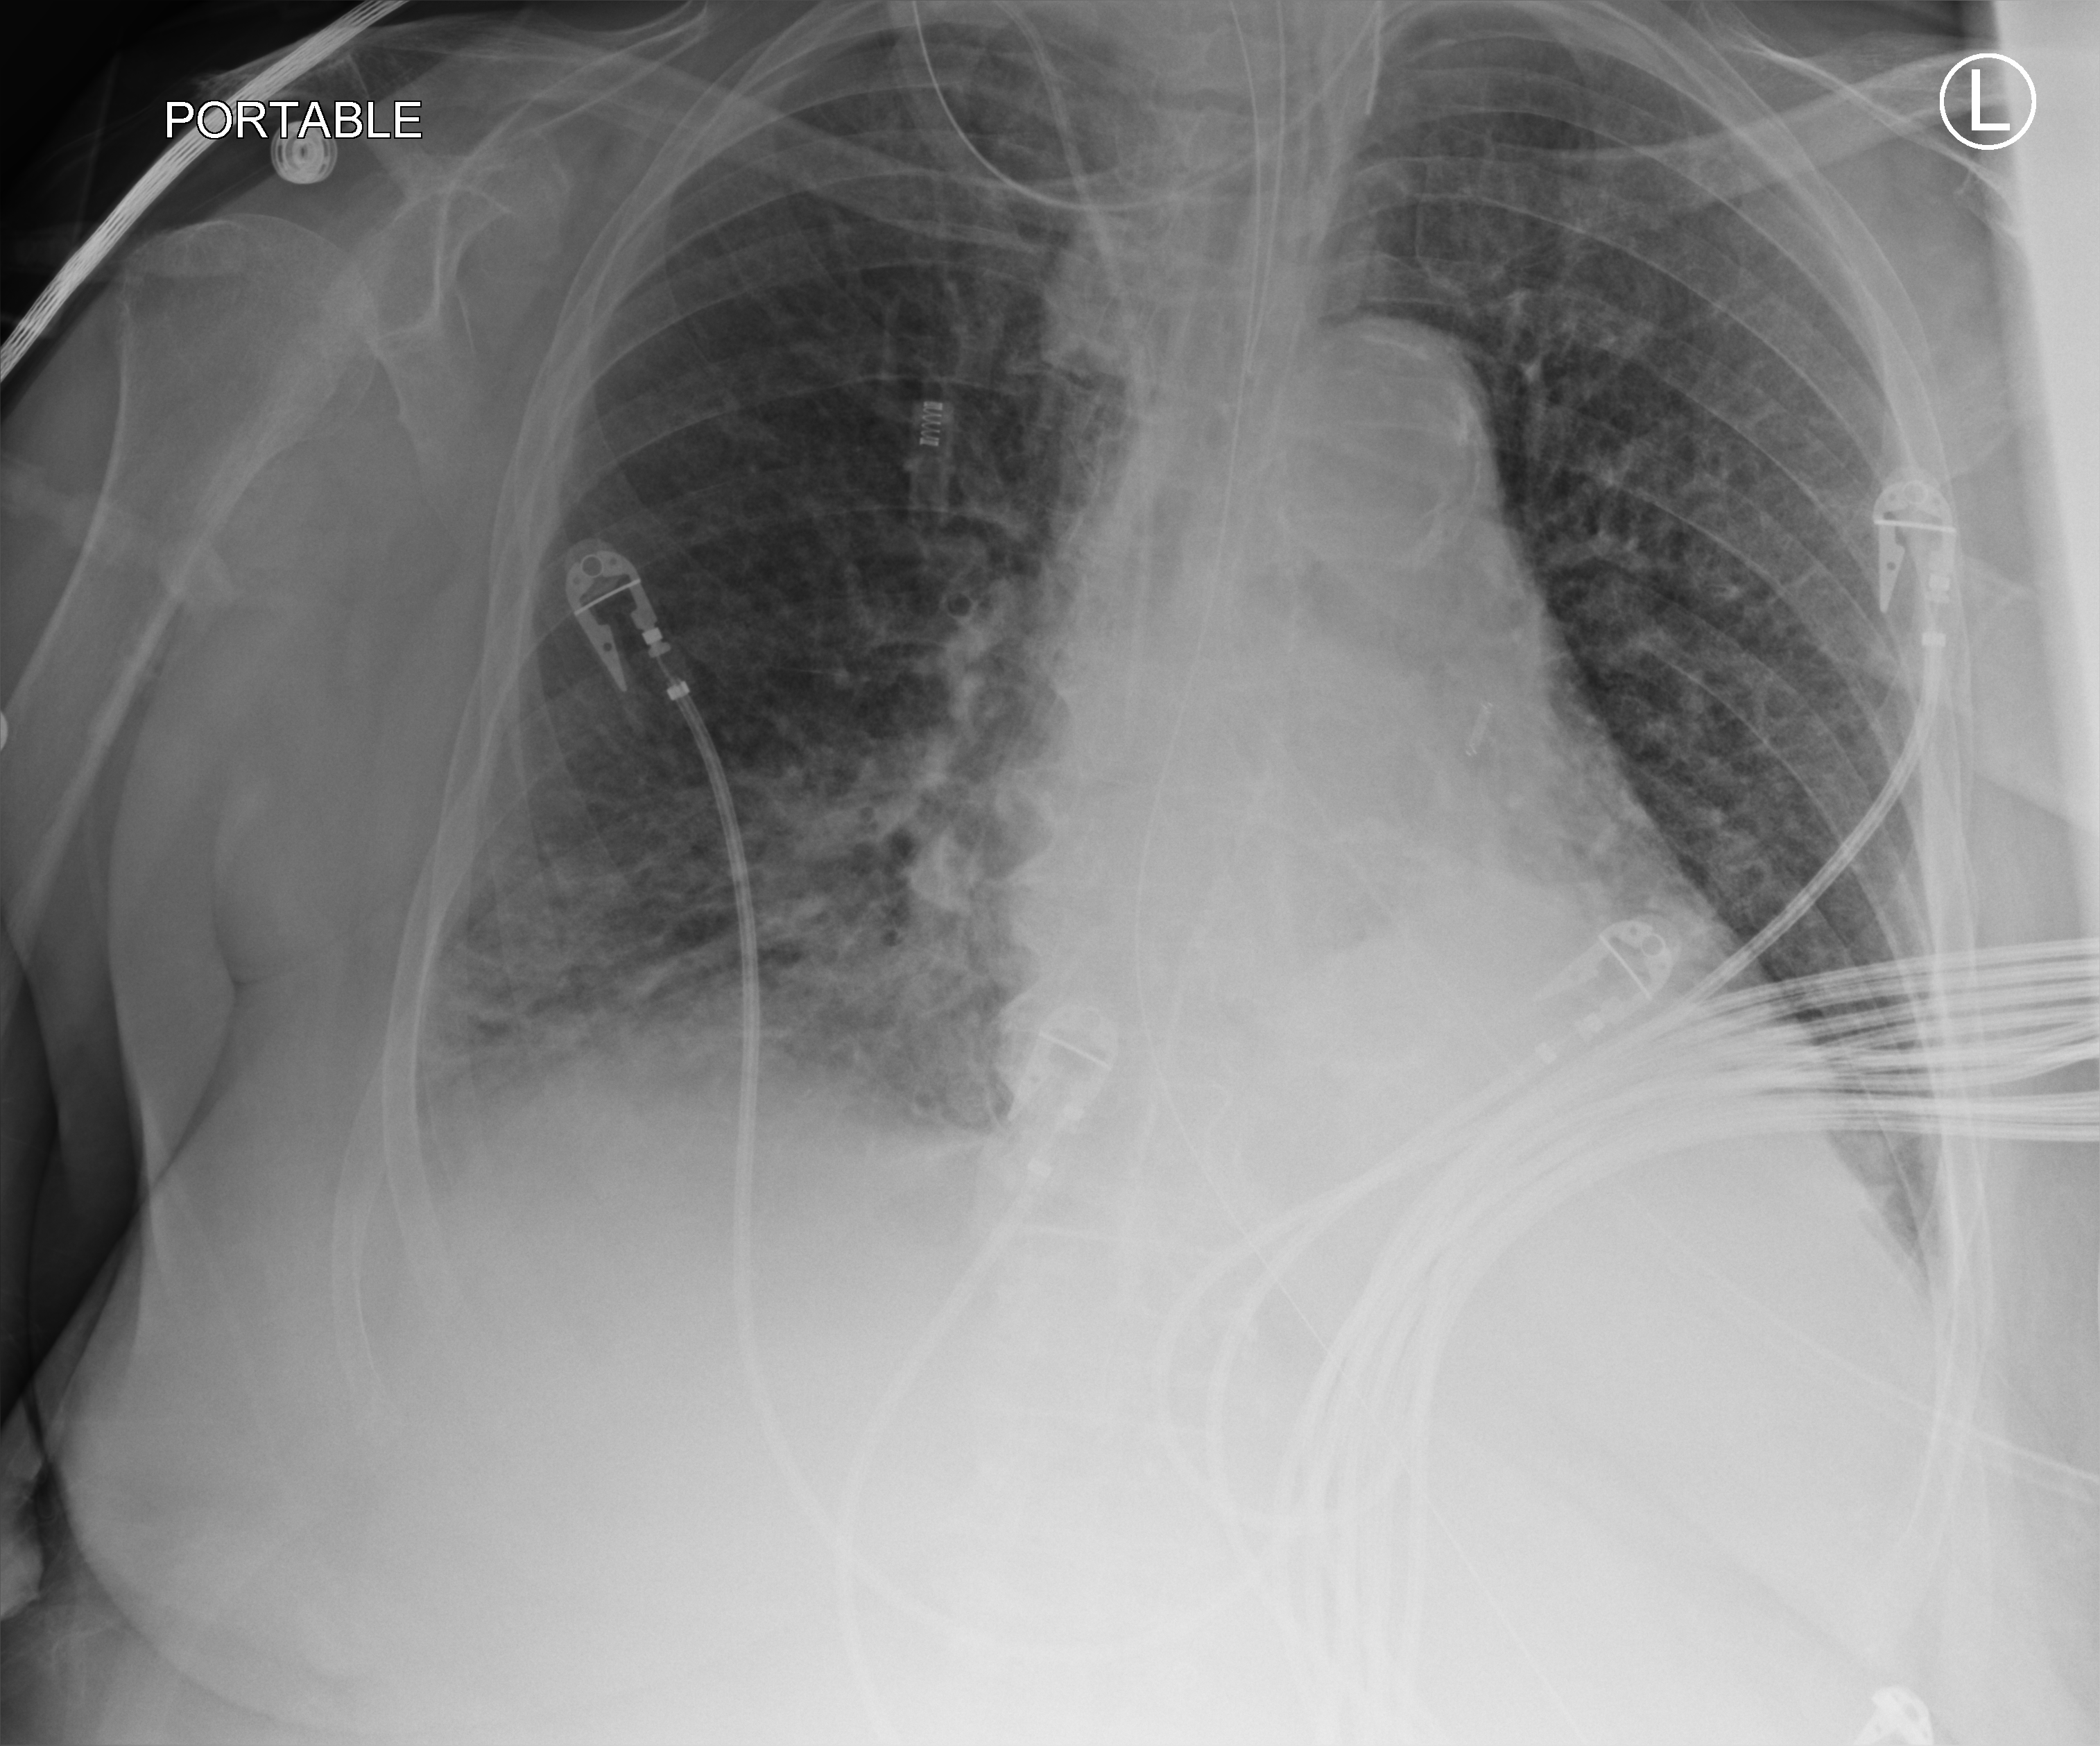
Portable chest radiograph; anteroposterior (AP) projection. Female patient hospitalised with COVID-19, age 75–90 years.
Hospital-stay facts (about this admission, not read from this image; timing relative to this image not recorded):
- chronic kidney disease (admission record): yes